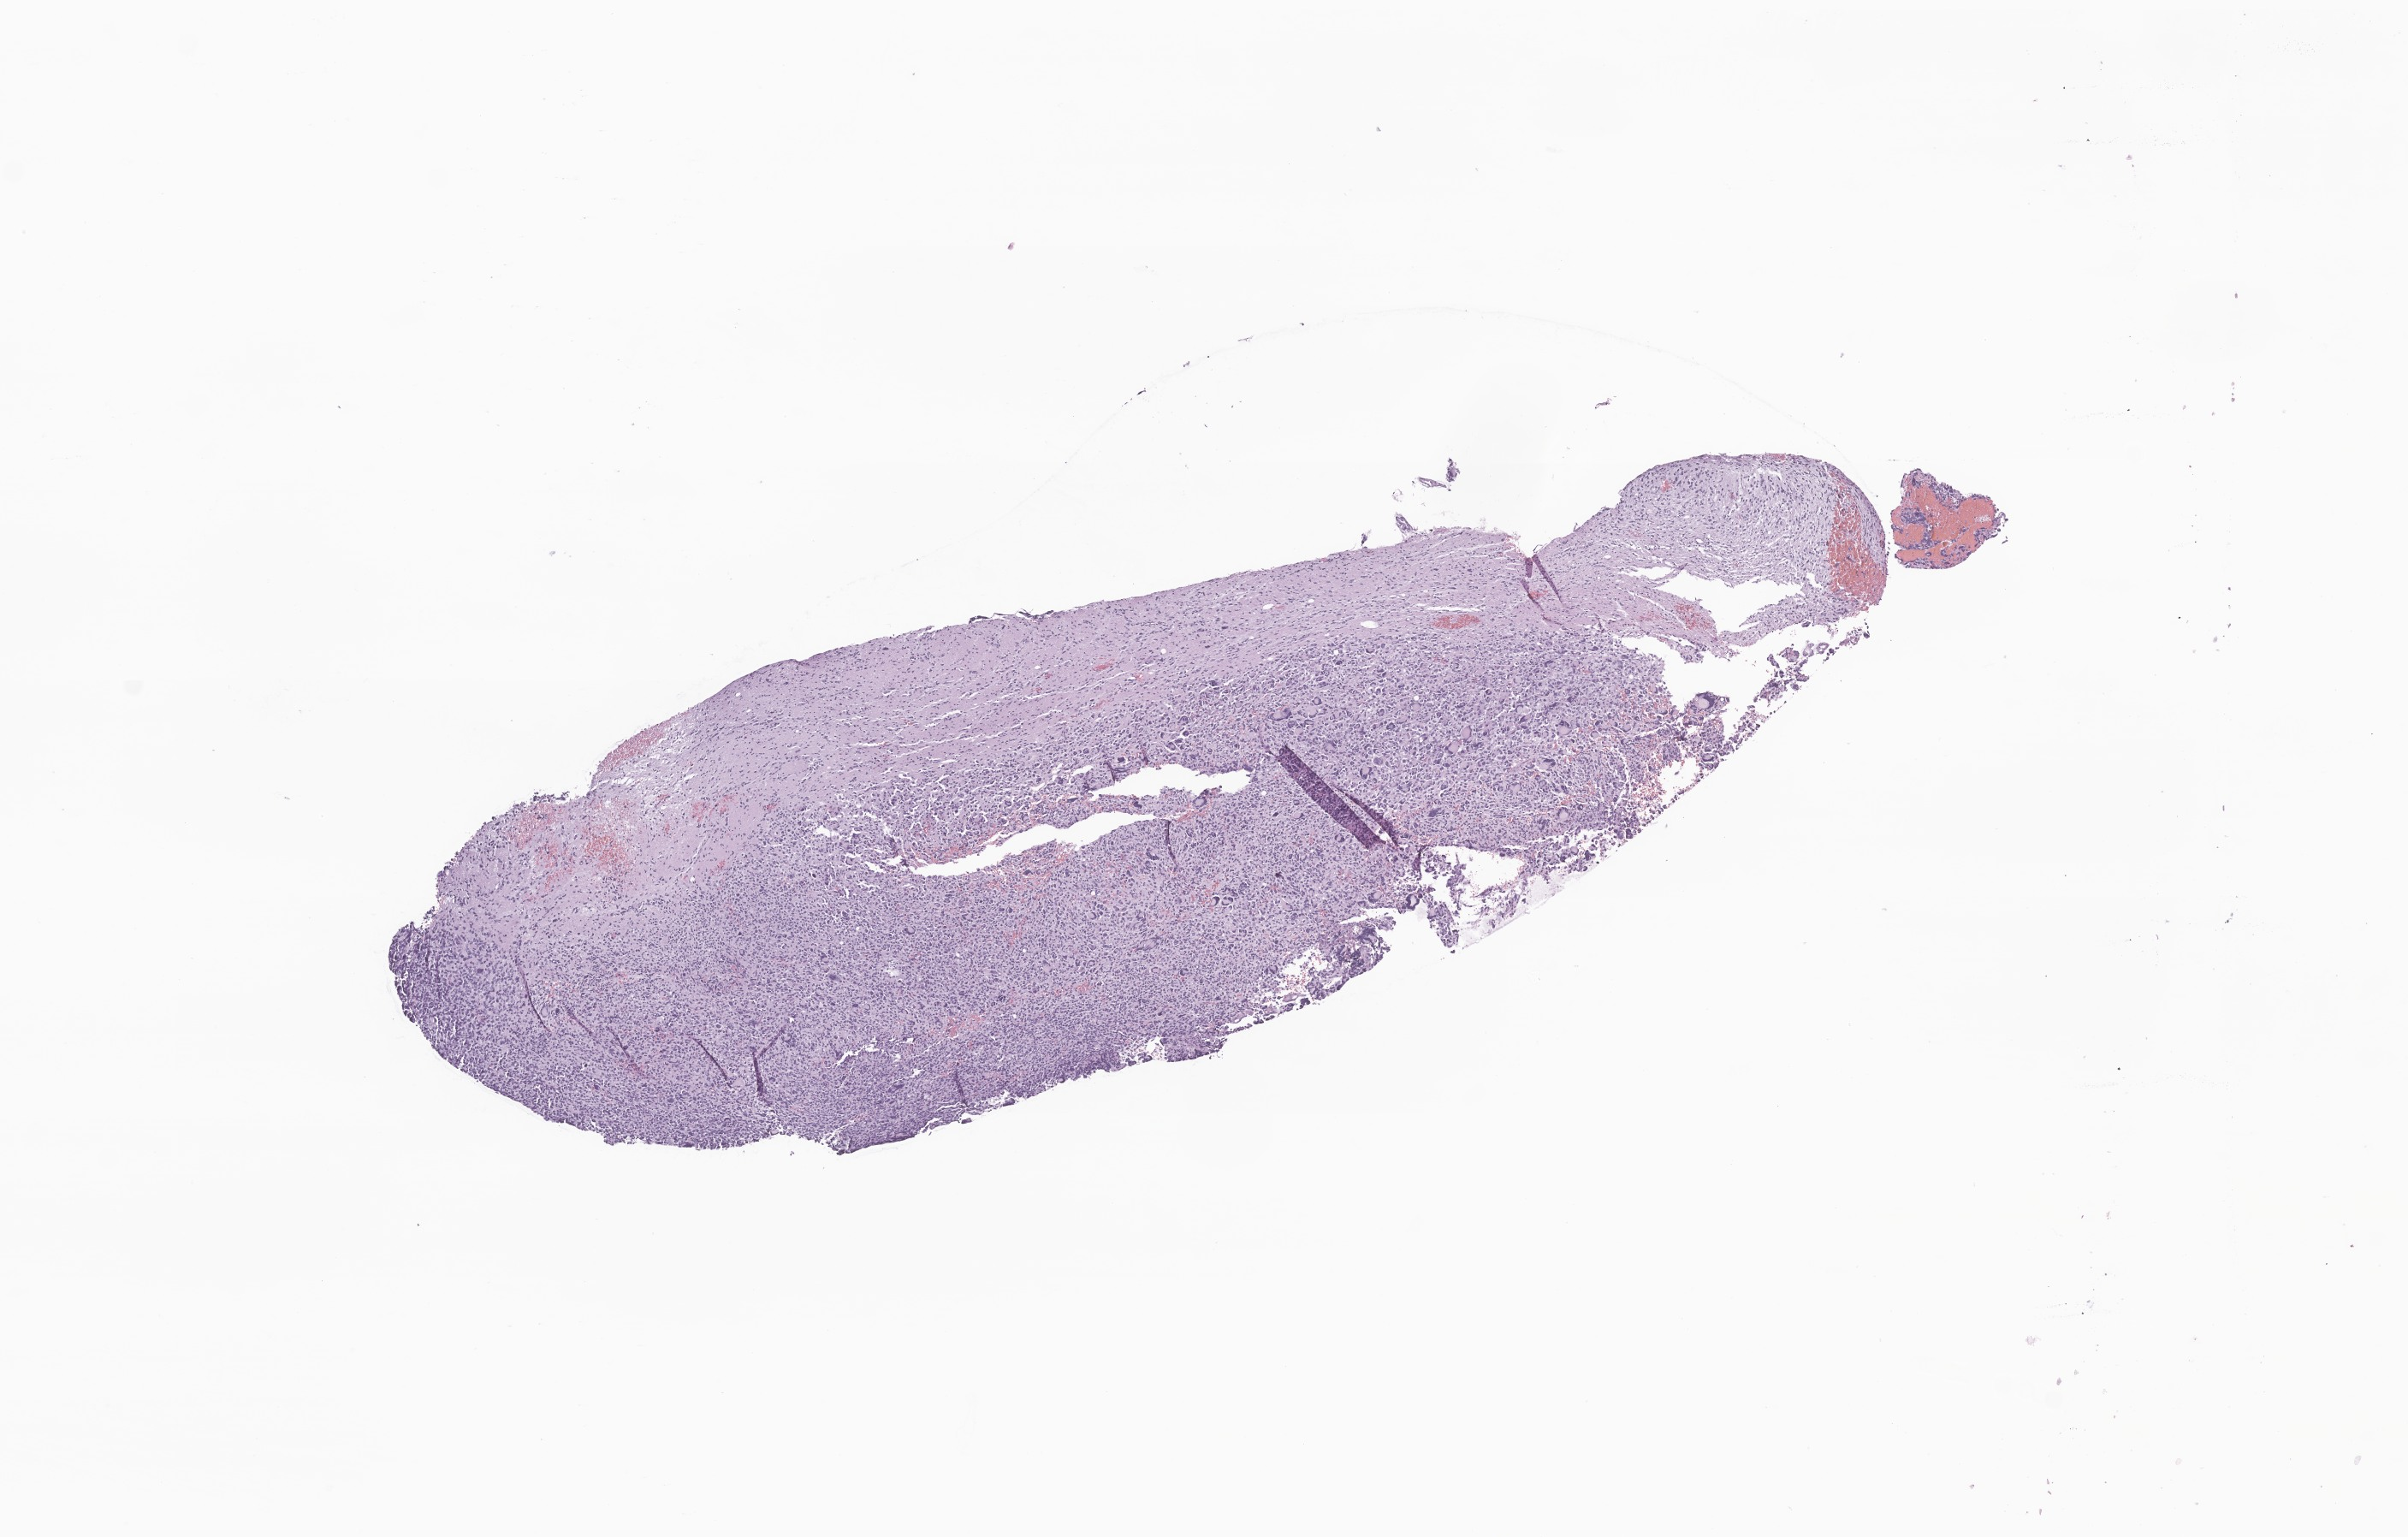
Digitized hematoxylin and eosin (H&E)-stained section of tumor tissue from the brain stem, shown as a low-resolution overview of the whole scanned area (about 11.9 x 7.6 mm). Formalin-fixed paraffin-embedded section. Patient: female, age 68 months (5 years 8 months).
Diagnosis (ICD-O-3 morphology term): Glioma, malignant.